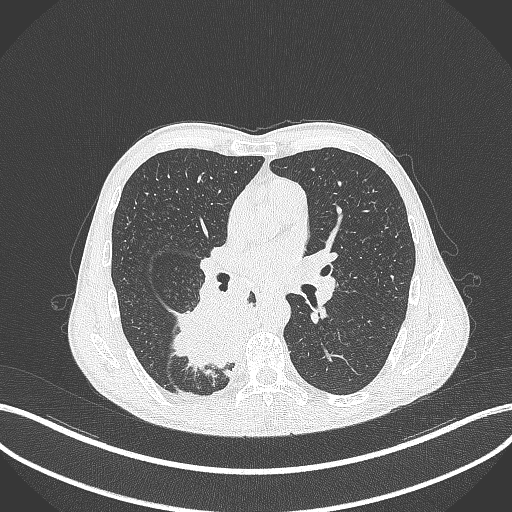
Chest CT, one axial slice. Slice 201 of 371 in the series (ordered by position). Reconstruction kernel B70f. 120 kVp. Lung window (W 1500 / L -600 HU). 1 mm slice thickness. 512 × 512 image matrix. Patient: male, 58 years. From the clinical record (not read from this slice): clinical TNM (as recorded): T3 N1 M1.
Structures marked on this image (bounding box drawn by a radiologist):
- lung tumour (recorded histology: squamous cell carcinoma): bounding box (x1, y1, x2, y2) in pixels: (169, 283, 255, 377)